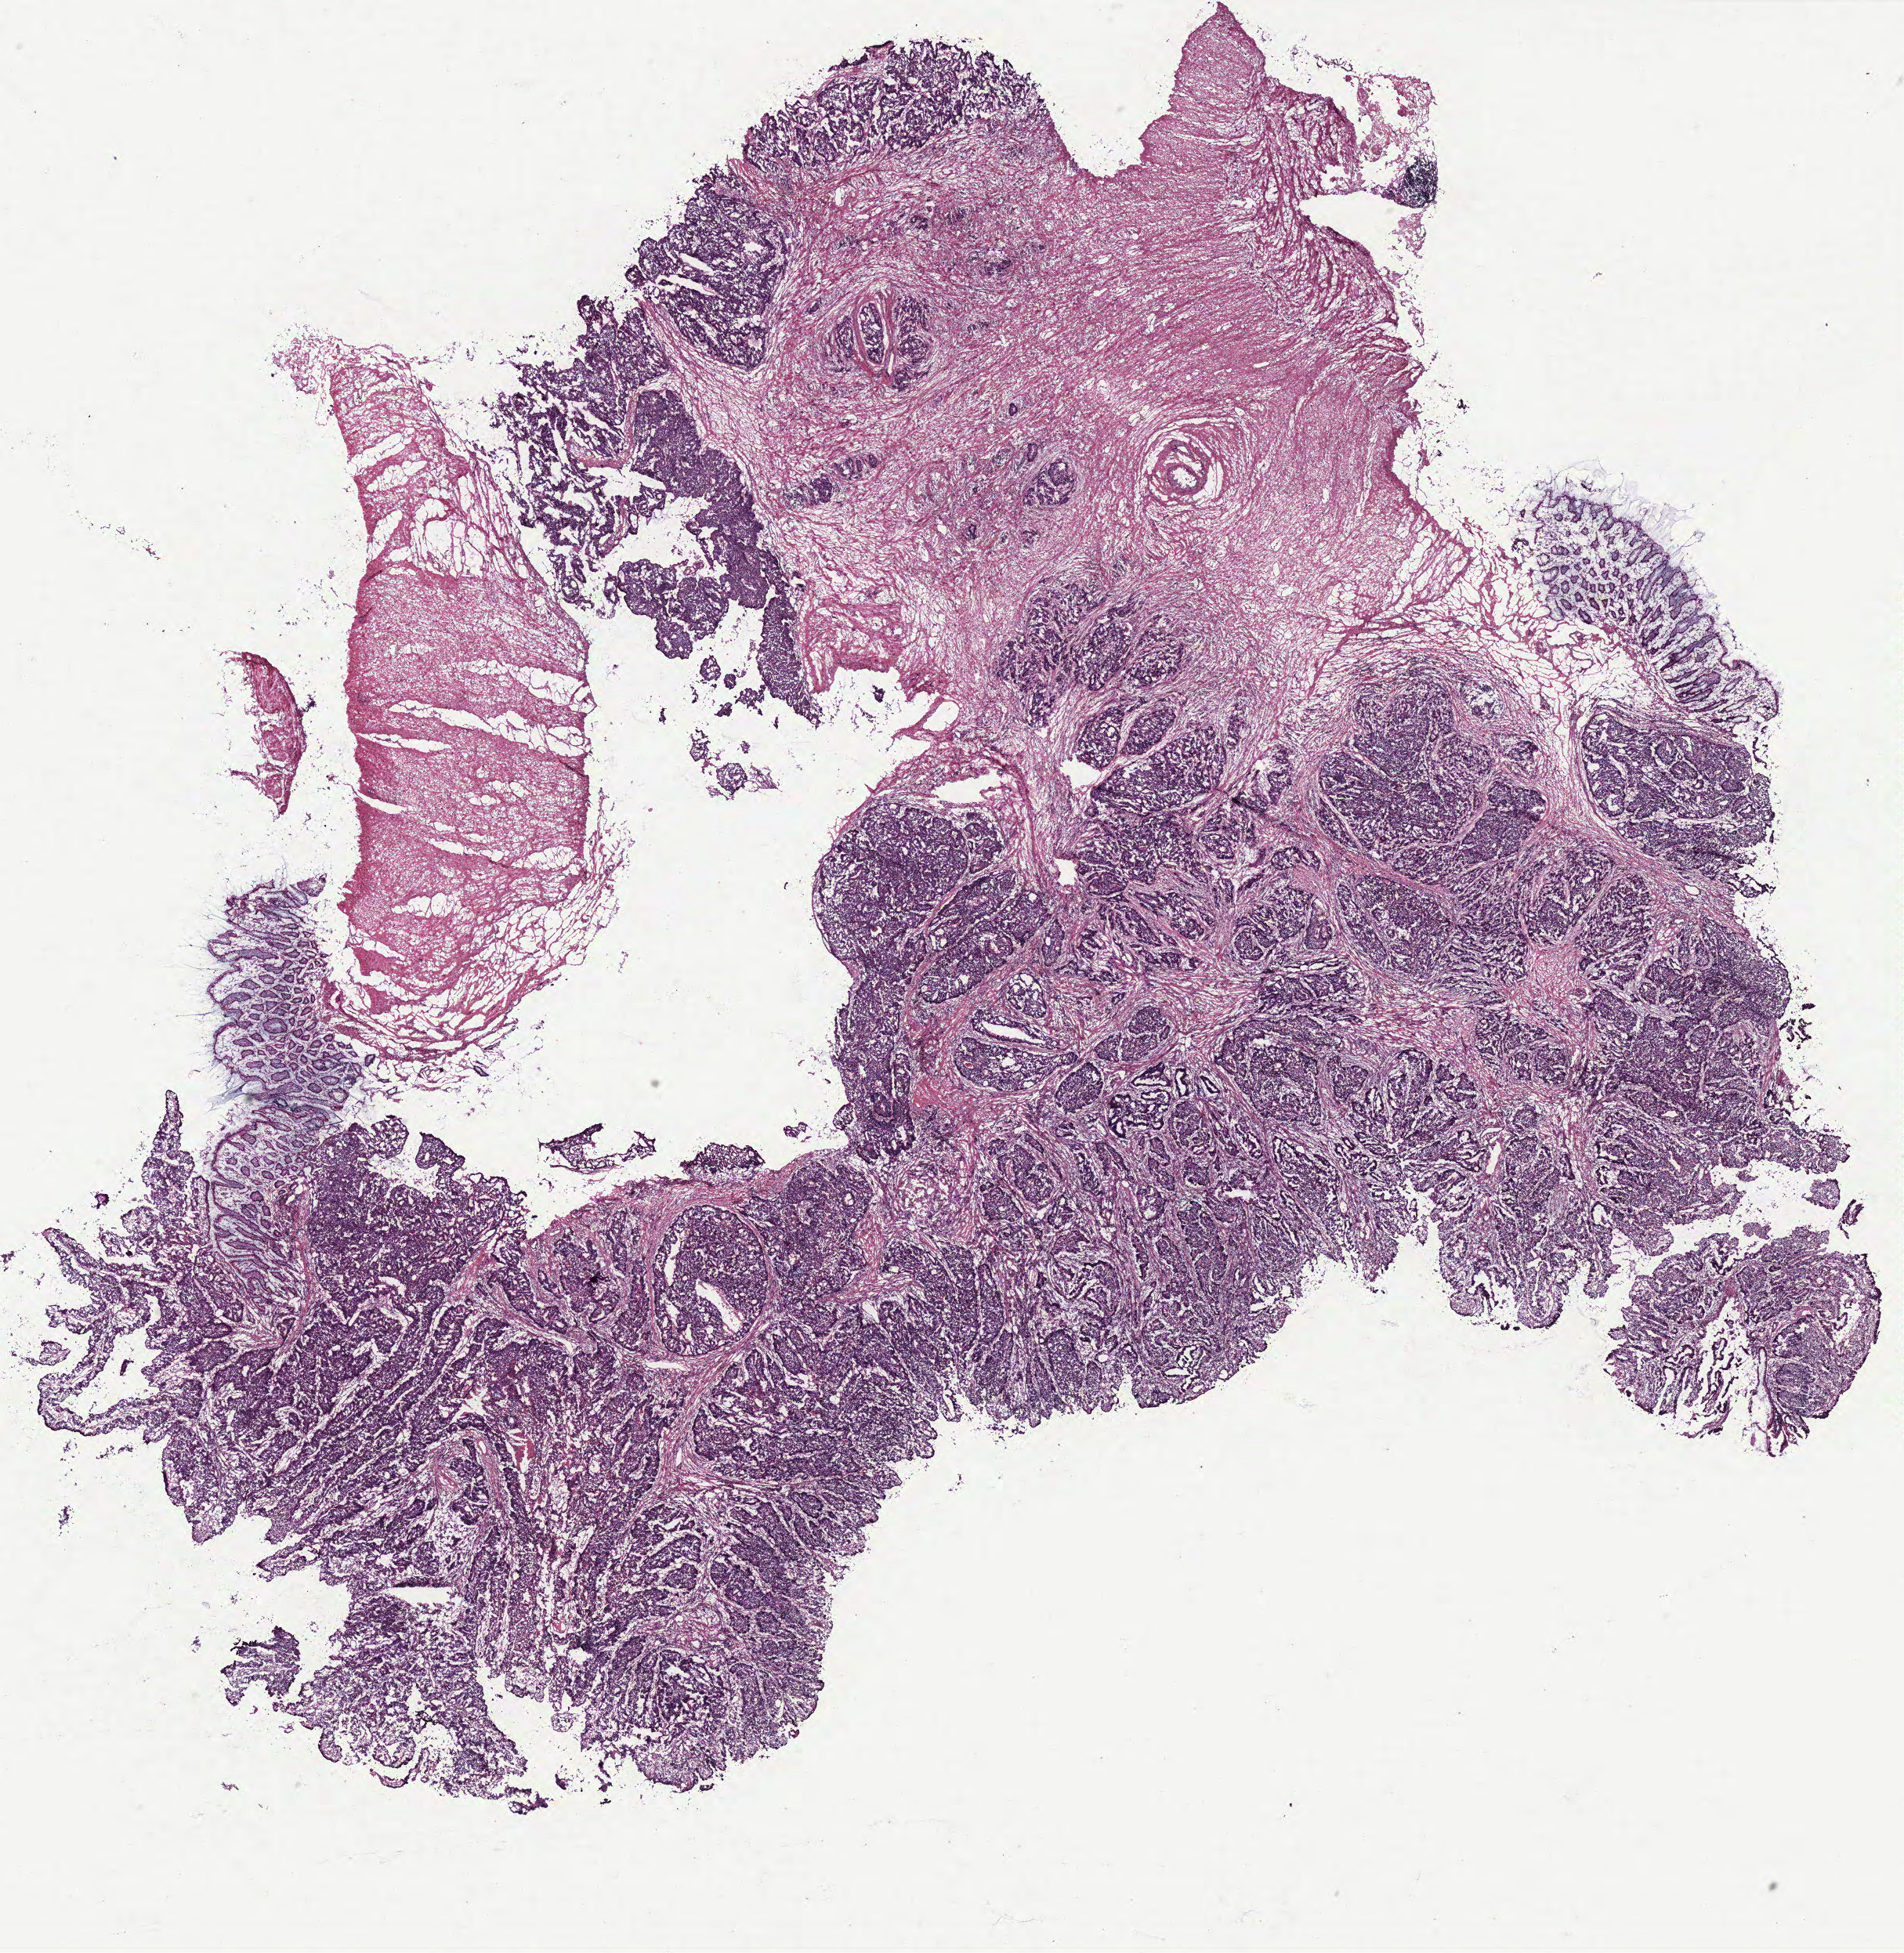
Whole-slide histology image, Hematoxylin and eosin (H&E) stained — low-resolution overview of the scanned area, about 19.4 x 20.0 mm. Tumour tissue sample, colon. Female, 67 y/o.
- diagnosis: Adenocarcinoma, NOS
- primary tumour site (as recorded): colon
- AJCC pathologic stage: IIA